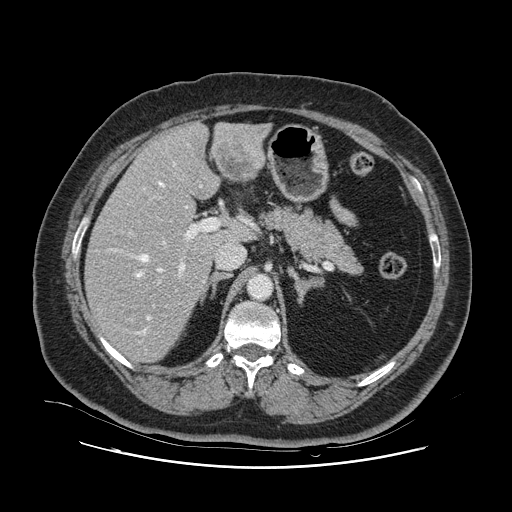
Contrast-enhanced abdominal CT, one axial slice; slice 66 of 132 in the series (ordered by position); intravenous contrast given; soft-tissue window (W 400 / L 40 HU); 2.5 mm slice thickness; 512 × 512 image matrix, field of view 391 × 391 mm. Female patient, age 73 years. From the clinical record (not read from this slice): diagnosis: colorectal cancer liver metastases, imaged before liver resection; multiple liver metastases: no; largest metastasis: 7 cm.
Annotated regions visible in this slice (outlined manually by an expert reader):
- hepatic veins: bounding box [x1, y1, x2, y2] px = [110, 162, 202, 335]
- liver: [86, 123, 267, 361]
- planned liver remnant (the part of the liver to remain after resection): [86, 150, 237, 361]
- portal vein (with intrahepatic branches): [130, 218, 219, 275]
- liver metastasis: [218, 145, 258, 176]